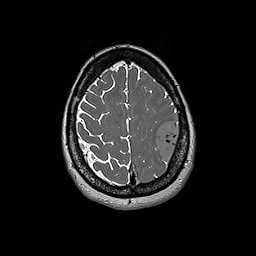
Brain MRI from a brain-tumour surgery series, one axial slice; position 55 of 192 along the scan axis; 256 × 256 image matrix, field of view 250 × 250 mm. From the clinical record (not read from this slice): histopathology: Glioblastoma; WHO grade: 4; IDH mutation: no; tumour location: Left Frontal.
Structures marked on this image (expert manual segmentation):
- tumour: bounding box <155,120,183,166> (left, top, right, bottom; pixels)